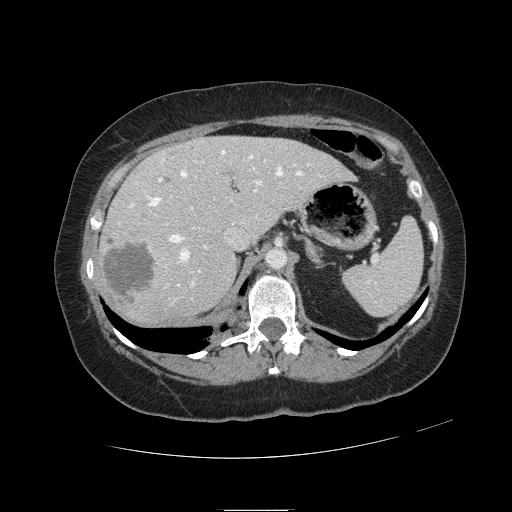
Contrast-enhanced abdominal CT, one axial slice; 120 kVp; intravenous contrast given; soft-tissue window (W 400 / L 40 HU); 2.5 mm slice thickness; 512 × 512 image matrix, field of view 400 × 400 mm. Female patient, age 52 years. Case-level facts recorded for this patient, not image findings: diagnosis: colorectal cancer liver metastases, imaged before liver resection; multiple liver metastases: yes; largest metastasis: 6.3 cm; chemotherapy before resection: yes.
Outlined on this slice (expert manual segmentation):
- hepatic veins: bounding box (x1, y1, x2, y2) in pixels: (129, 151, 310, 299)
- liver: (100, 137, 351, 324)
- planned liver remnant (the part of the liver to remain after resection): (167, 137, 351, 236)
- portal vein (with intrahepatic branches): (119, 160, 266, 287)
- liver metastasis: (105, 246, 155, 304)